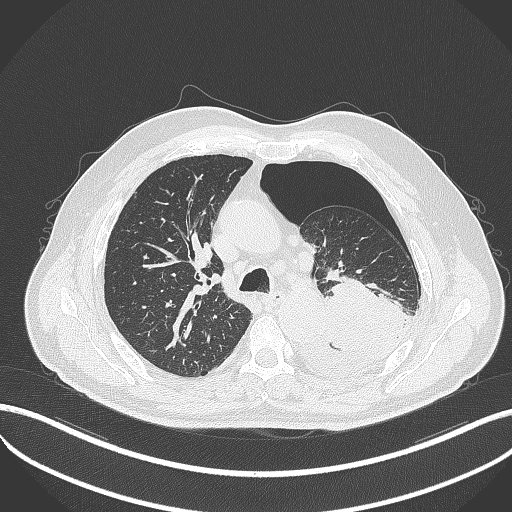
Chest CT, one axial slice. Slice 350 of 464 in the series (ordered by position). Reconstruction kernel B70f. Lung window (W 1500 / L -600 HU). 1 mm slice thickness. 512 × 512 image matrix, field of view 400 × 400 mm. Male patient, age 76 years. From the clinical record (not read from this slice): clinical TNM (as recorded): T3 N0 M1b.
Structures marked on this image (rectangle marked by the reading radiologist):
- lung tumour (recorded histology: adenocarcinoma): box from (x=323, y=279) to (x=410, y=350) px